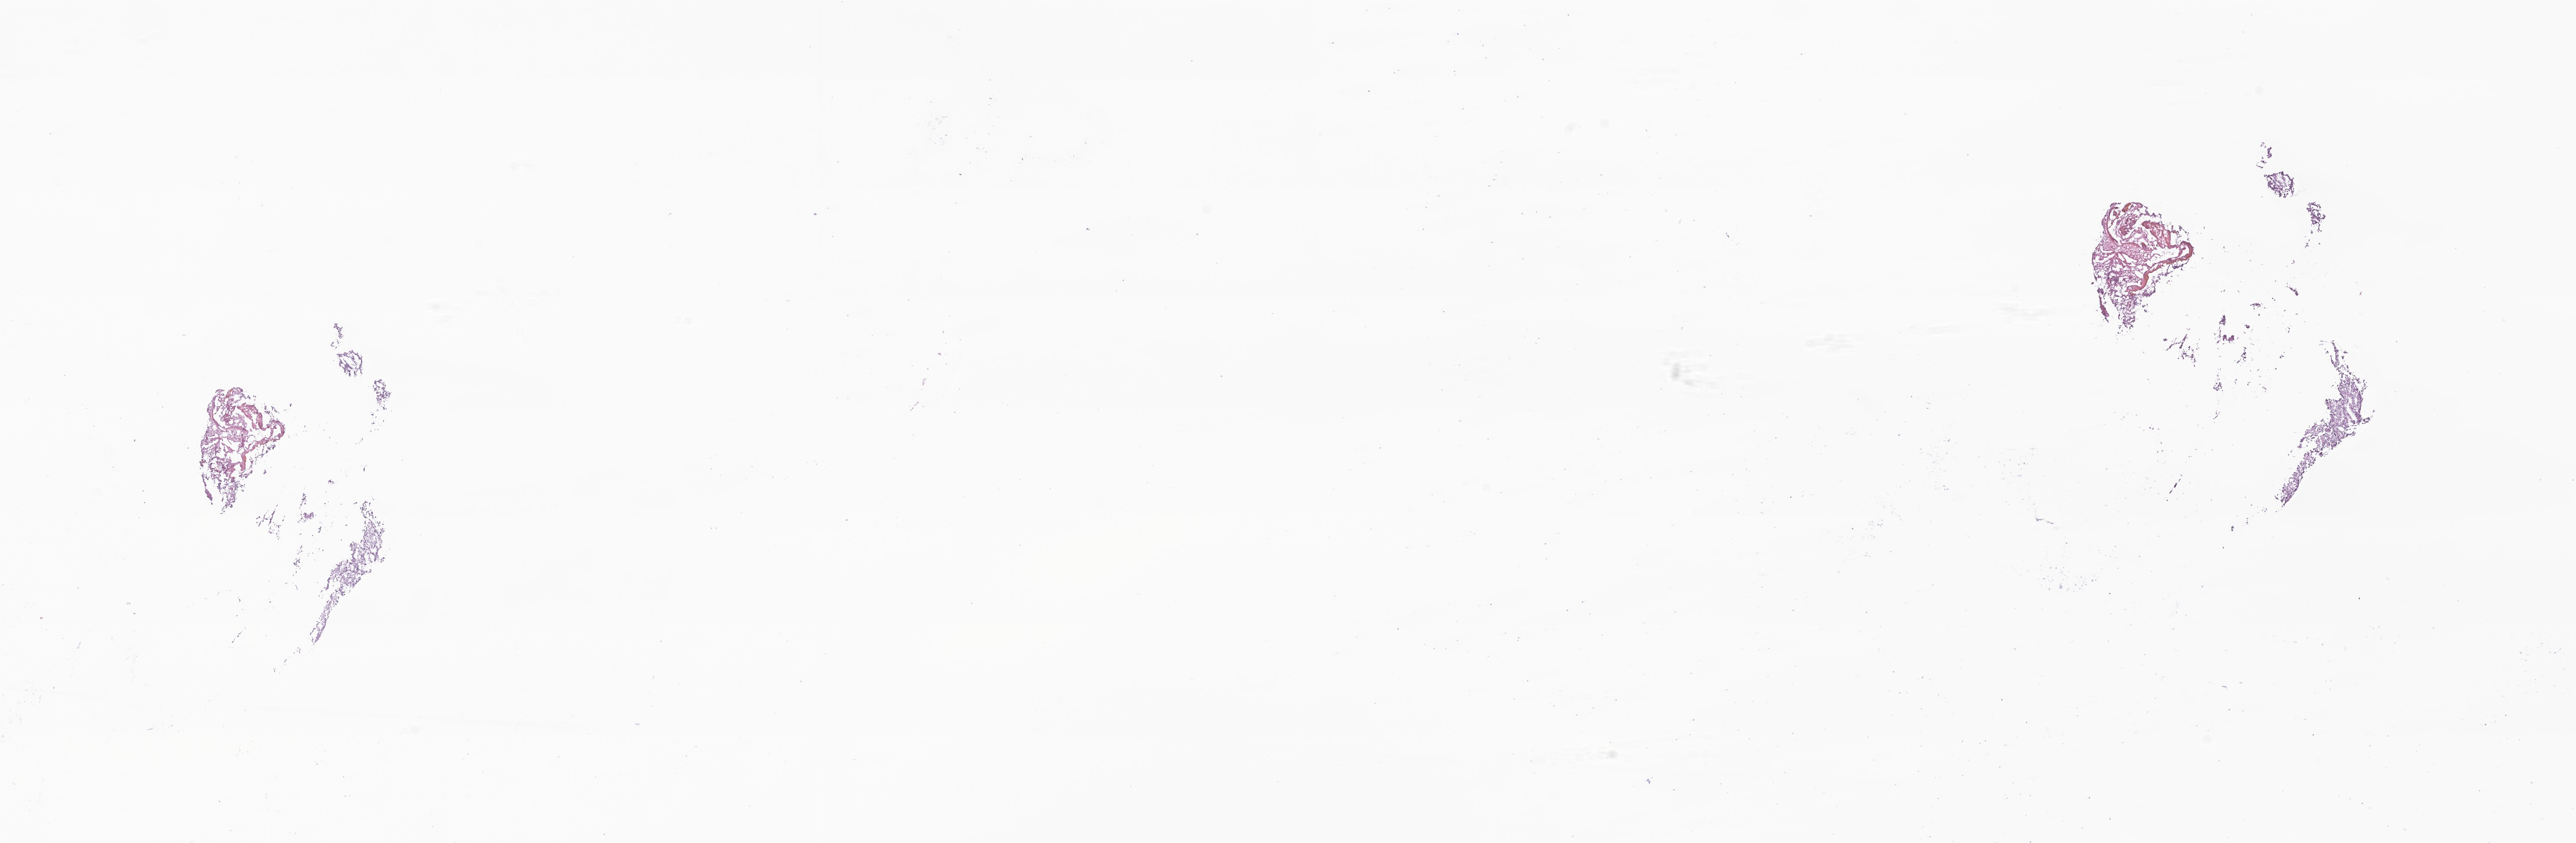
Digitized hematoxylin and eosin (H&E)-stained section of tumor tissue from the pineal gland, a low-resolution overview of the entire scanned area, about 25.1 x 8.2 mm. Frozen section. Patient male; age 220 months (18 years 4 months).
Diagnosis (ICD-O-3 morphology term): Neoplasm, uncertain whether benign or malignant.